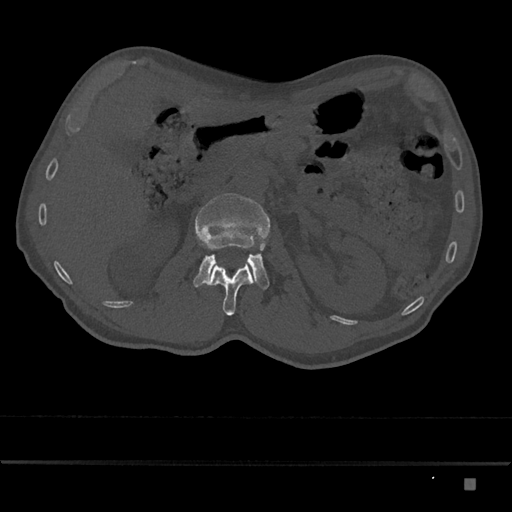
CT including the spine, one axial slice. 120 kVp. Bone window (W 1800 / L 400 HU). 0.5 mm slice thickness. 512 × 512 image matrix. Male patient, age 72 years. Case-level facts recorded for this patient, not image findings: primary cancer: prostate.
Structures marked on this image (semi-automatic segmentation, software-assisted and operator-edited):
- L1 vertebra: bounding box [x1, y1, x2, y2] px = [206, 262, 255, 316]
- L2 vertebra: [193, 193, 270, 289]